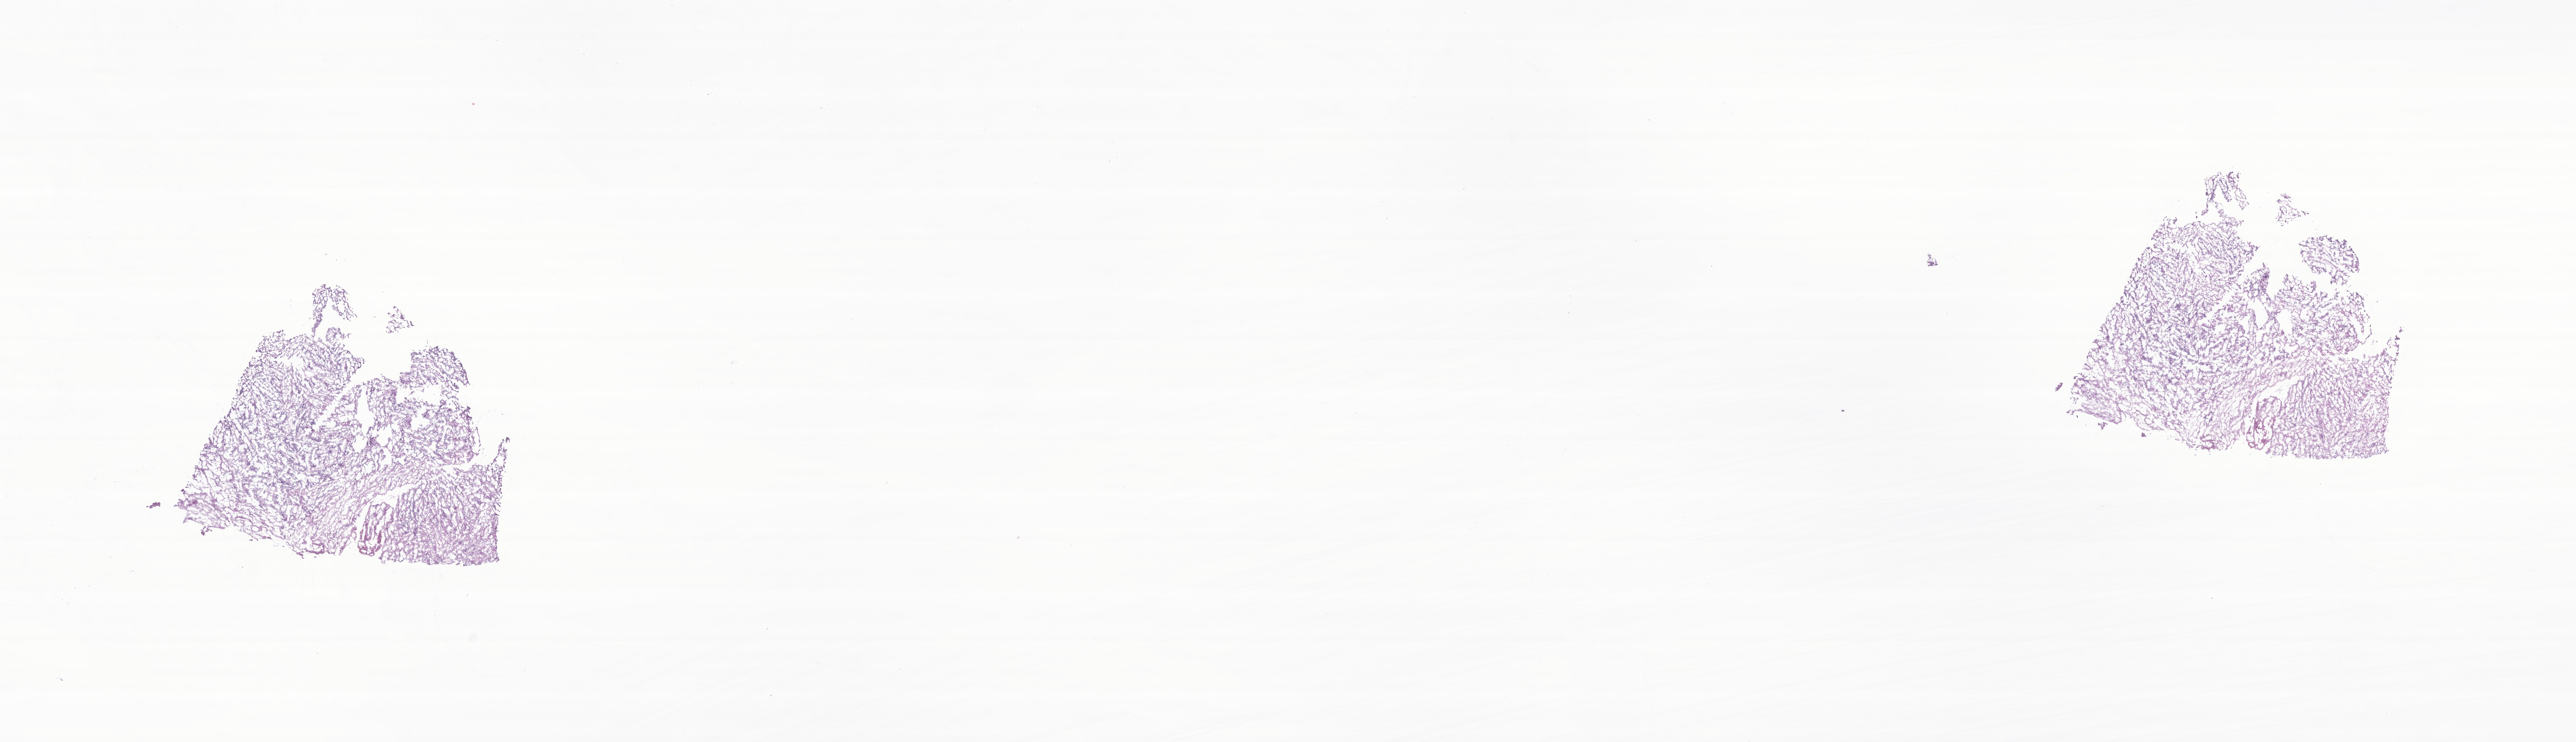
Haematoxylin and eosin whole-slide image of tumor tissue from the brain, low-resolution overview of the scanned area, about 27.4 x 7.9 mm, cryosection (OCT / tissue freezing medium). Patient: male, age 600 days (about 1.6 years).
Recorded diagnosis: Ependymoma, NOS.